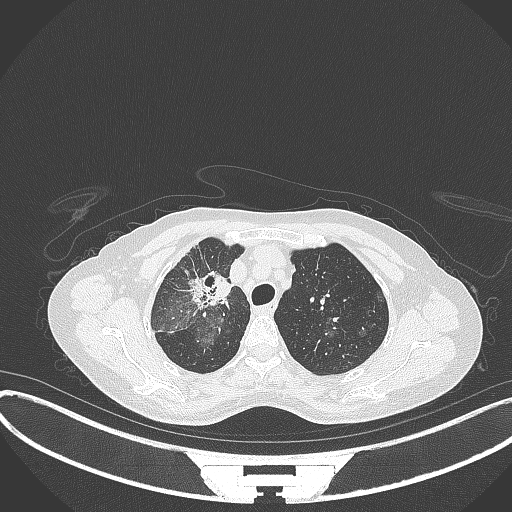
Chest CT, one axial slice. Slice 252 of 284 in the series (ordered by position). Reconstruction kernel B70f. Lung window (W 1500 / L -600 HU). 1 mm slice thickness. 512 × 512 image matrix, field of view 400 × 400 mm. Female patient, age 59 years. From the clinical record (not read from this slice): clinical TNM (as recorded): T3 N0 M0.
Annotated regions visible in this slice (bounding box drawn by a radiologist):
- lung tumour (recorded histology: adenocarcinoma): bounding box <190,266,231,311> (left, top, right, bottom; pixels)